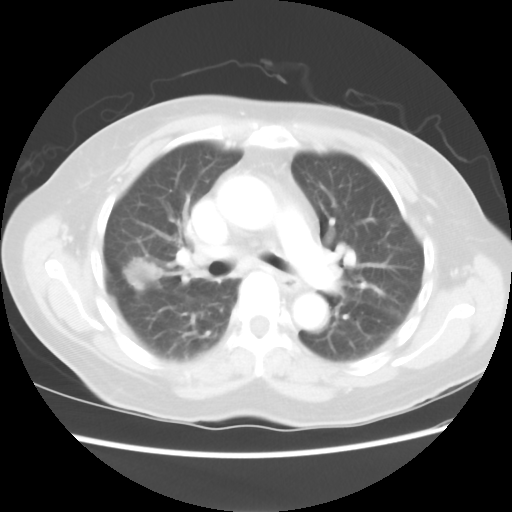
Chest CT, one axial slice. Position 43 of 80 along the scan axis. Reconstruction kernel STANDARD. 100 kVp. Lung window (W 1500 / L -600 HU). 512 × 512 image matrix. Patient: female, 67 years. Case-level facts recorded for this patient, not image findings: clinical TNM (as recorded): T1c N1 M0.
Annotated regions visible in this slice (bounding box drawn by a radiologist):
- lung tumour (recorded histology: adenocarcinoma): bounding box [x1, y1, x2, y2] px = [116, 252, 173, 300]